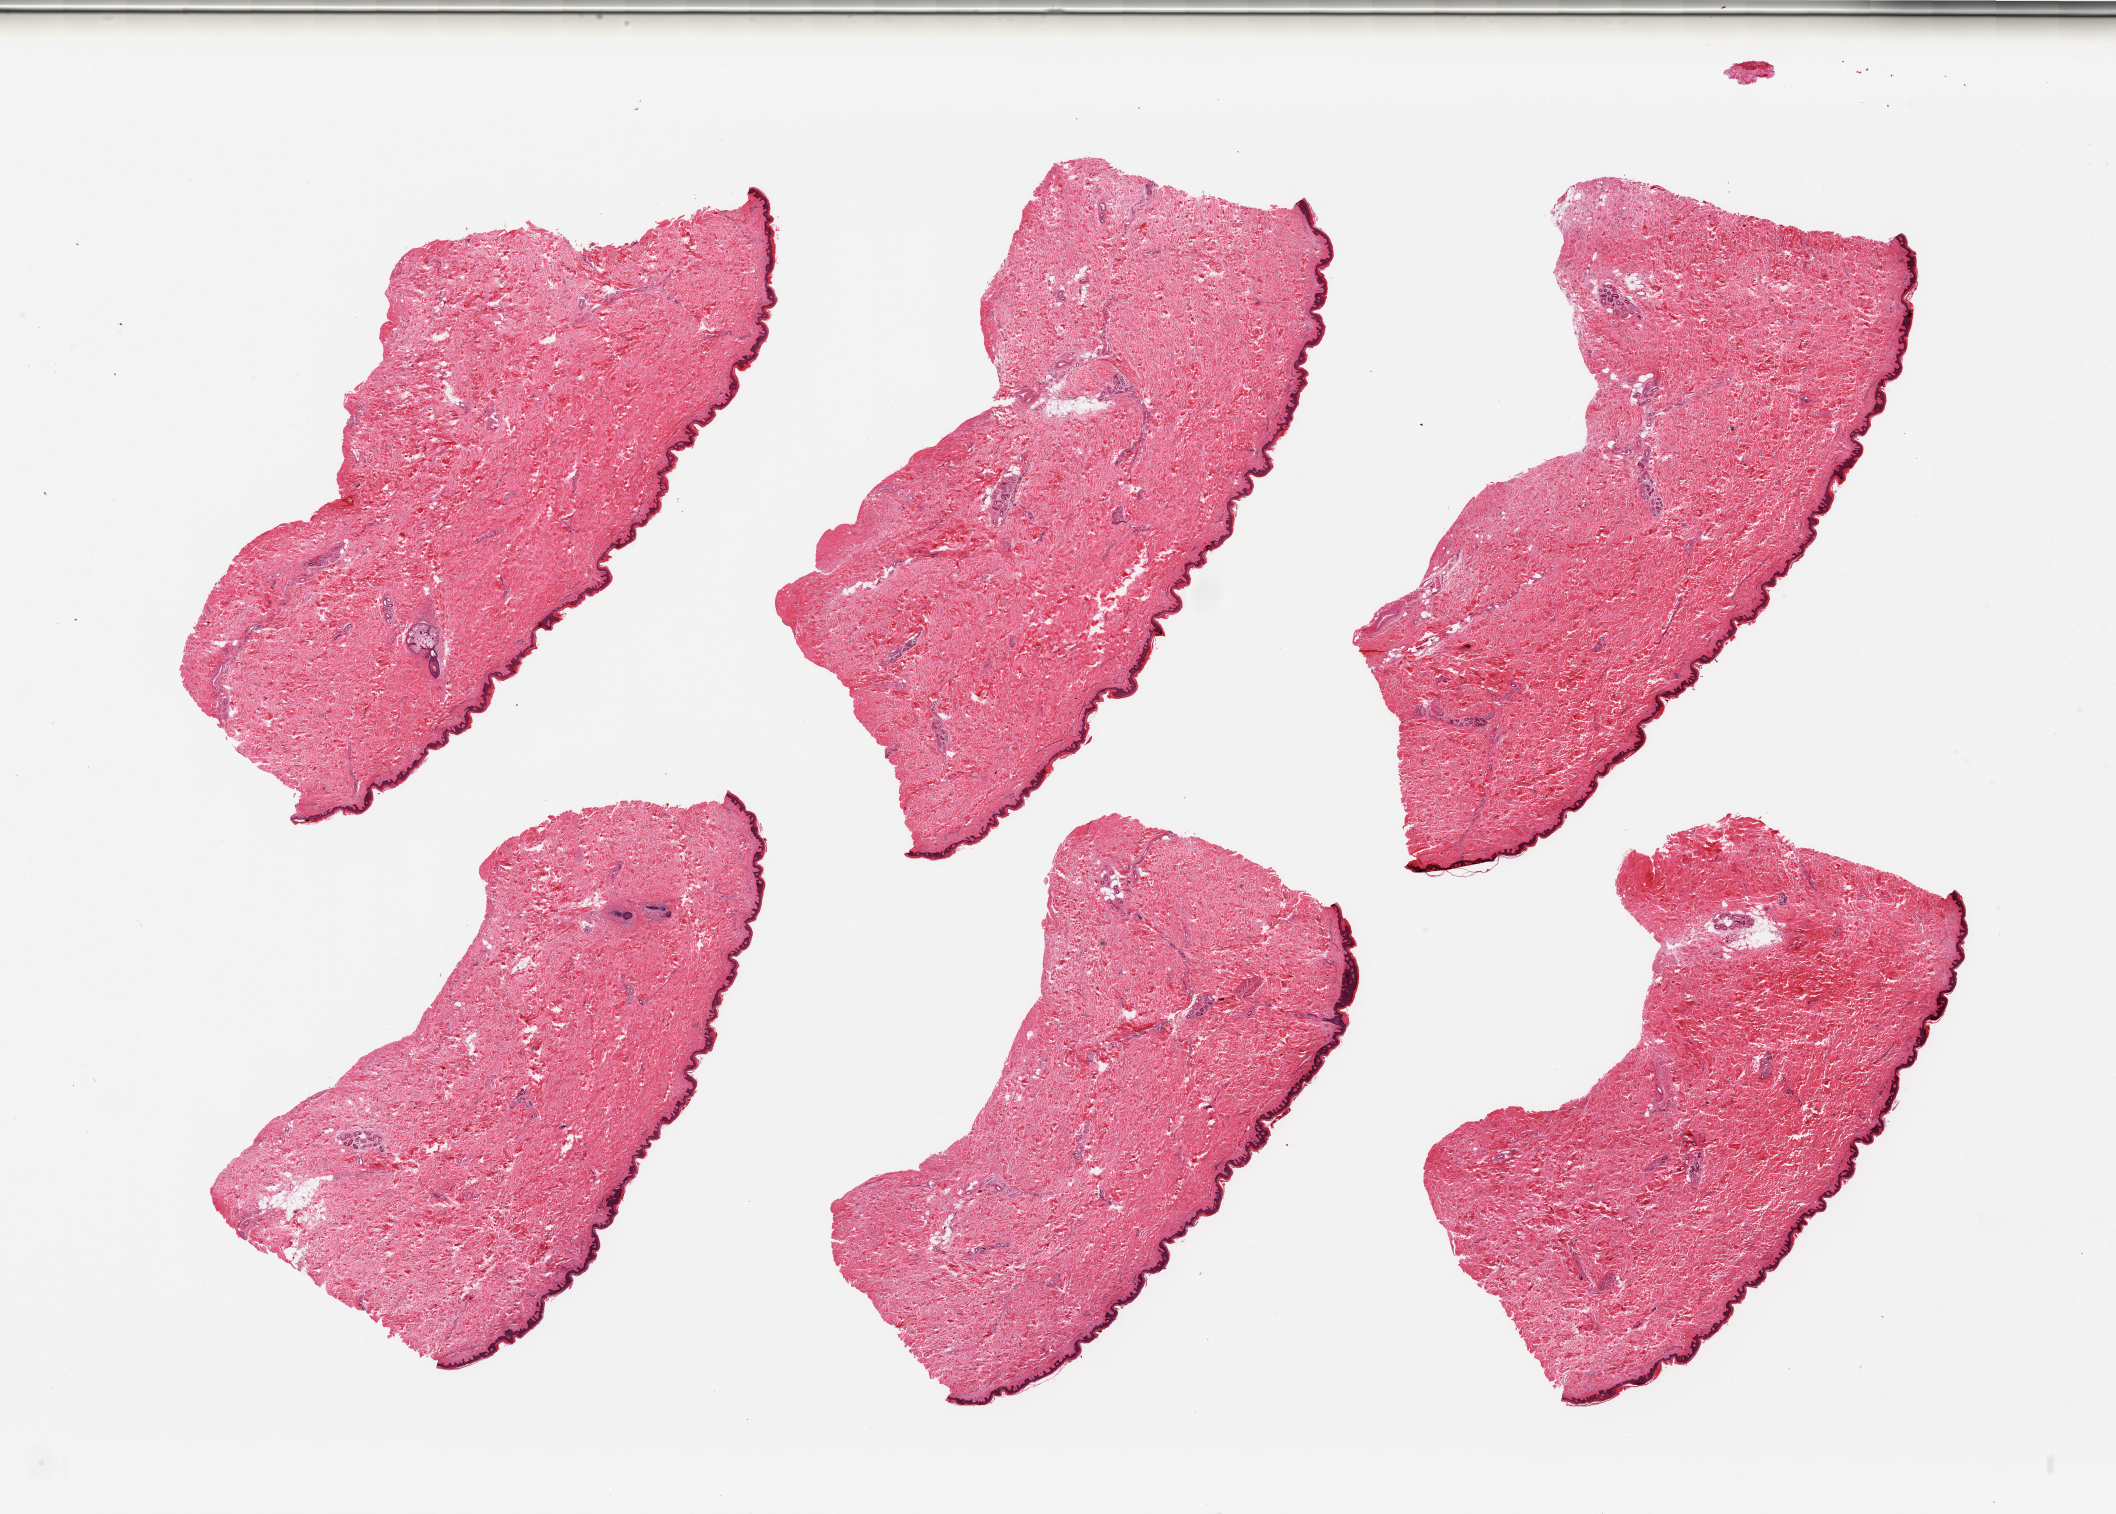
Hematoxylin and eosin (H&E) whole-slide image, brightfield — low-resolution overview of the scanned area, about 33.5 x 23.9 mm, PAXgene-fixed paraffin-embedded (PFPE) section, sampled site (target tissue): skin of suprapubic region, tissue donor sample. Male donor.
• review note (as recorded): 6 pieces; well trimmed skin with rare hair follicles